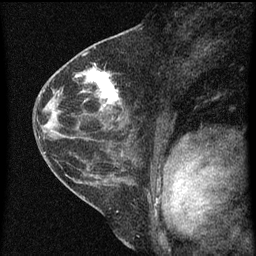
Breast MRI (dynamic contrast-enhanced), one sagittal slice. Slice 32 of 60 in the series (ordered by position). Dynamic contrast-enhanced series, image 2 of 3 at this slice position (ordered by acquisition). 1.5 T. TE 4.2 ms, TR 8 ms. 2 mm slice thickness. 256 × 256 image matrix, field of view 180 × 180 mm. Patient: female, 48 years.
Structures marked on this image (semi-automatically segmented with operator editing):
- analysis volume of interest (the breast-tissue region the enhancement analysis was run in; not a lesion): bounding box <82,68,126,125> (left, top, right, bottom; pixels)
- tumour enhancement mask (voxels above the 70 % enhancement threshold inside the analysis volume of interest): <87,70,119,111>